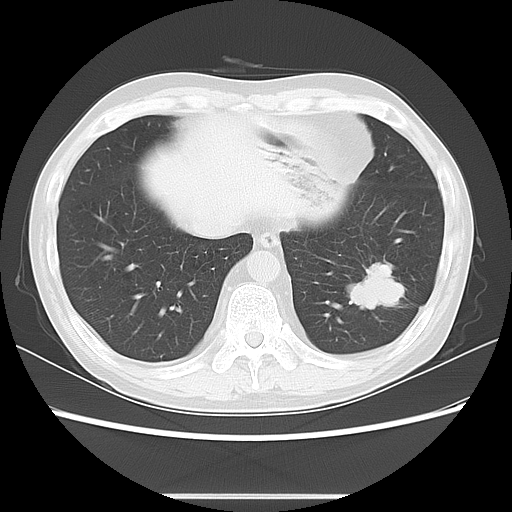
Chest CT, one axial slice. Position 22 of 63 along the scan axis. Reconstruction kernel LUNG. Lung window (W 1500 / L -600 HU). 5 mm slice thickness. 512 × 512 image matrix, field of view 347 × 347 mm. Male patient, age 49 years. From the clinical record (not read from this slice): clinical TNM (as recorded): T3 N0 M0.
Annotated regions visible in this slice (rectangle marked by the reading radiologist):
- lung tumour (recorded histology: squamous cell carcinoma): box from (x=337, y=250) to (x=416, y=321) px